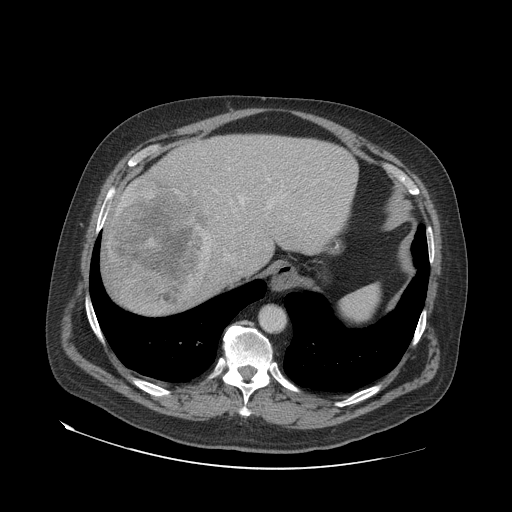
Contrast-enhanced abdominal CT (liver protocol), one axial slice; position 58 of 79 along the scan axis; 140 kVp; soft-tissue window (W 400 / L 40 HU); 2.5 mm slice thickness; 512 × 512 image matrix, field of view 480 × 480 mm. Case-level facts recorded for this patient, not image findings: diagnosis: hepatocellular carcinoma (patient treated with transarterial chemoembolisation; whether this scan precedes or follows treatment is not stated here); TNM stage (as recorded): Stage-IVA; Child-Pugh class: A.
Outlined on this slice (semi-automatic segmentation, software-assisted and operator-edited):
- abdominal aorta: bounding box (x1, y1, x2, y2) in pixels: (261, 306, 285, 330)
- liver parenchyma outside the tumour (the mass and vessels are separate outlines, so this box may not span the whole liver): (102, 134, 358, 314)
- mass: (106, 176, 211, 309)
- liver vessels: (240, 178, 274, 208)